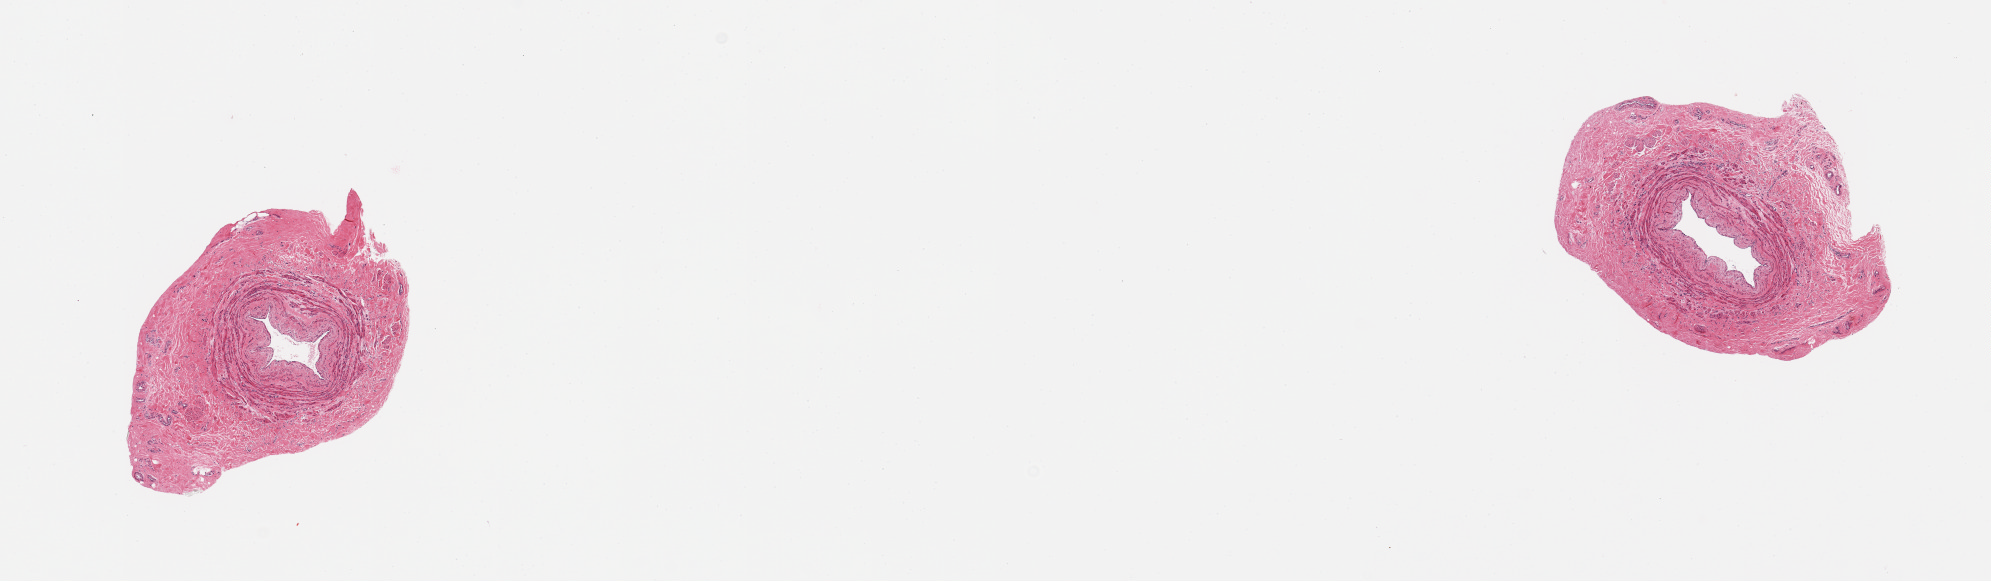
H&E whole-slide image — a low-resolution overview of the entire scanned area, about 15.8 x 4.6 mm (from a 20x scan). PAXgene-fixed paraffin-embedded (PFPE) section. Sampled site (target tissue): tibial artery. Donor tissue sample. Donor sex: male.
Review note (as recorded): 2 pieces.